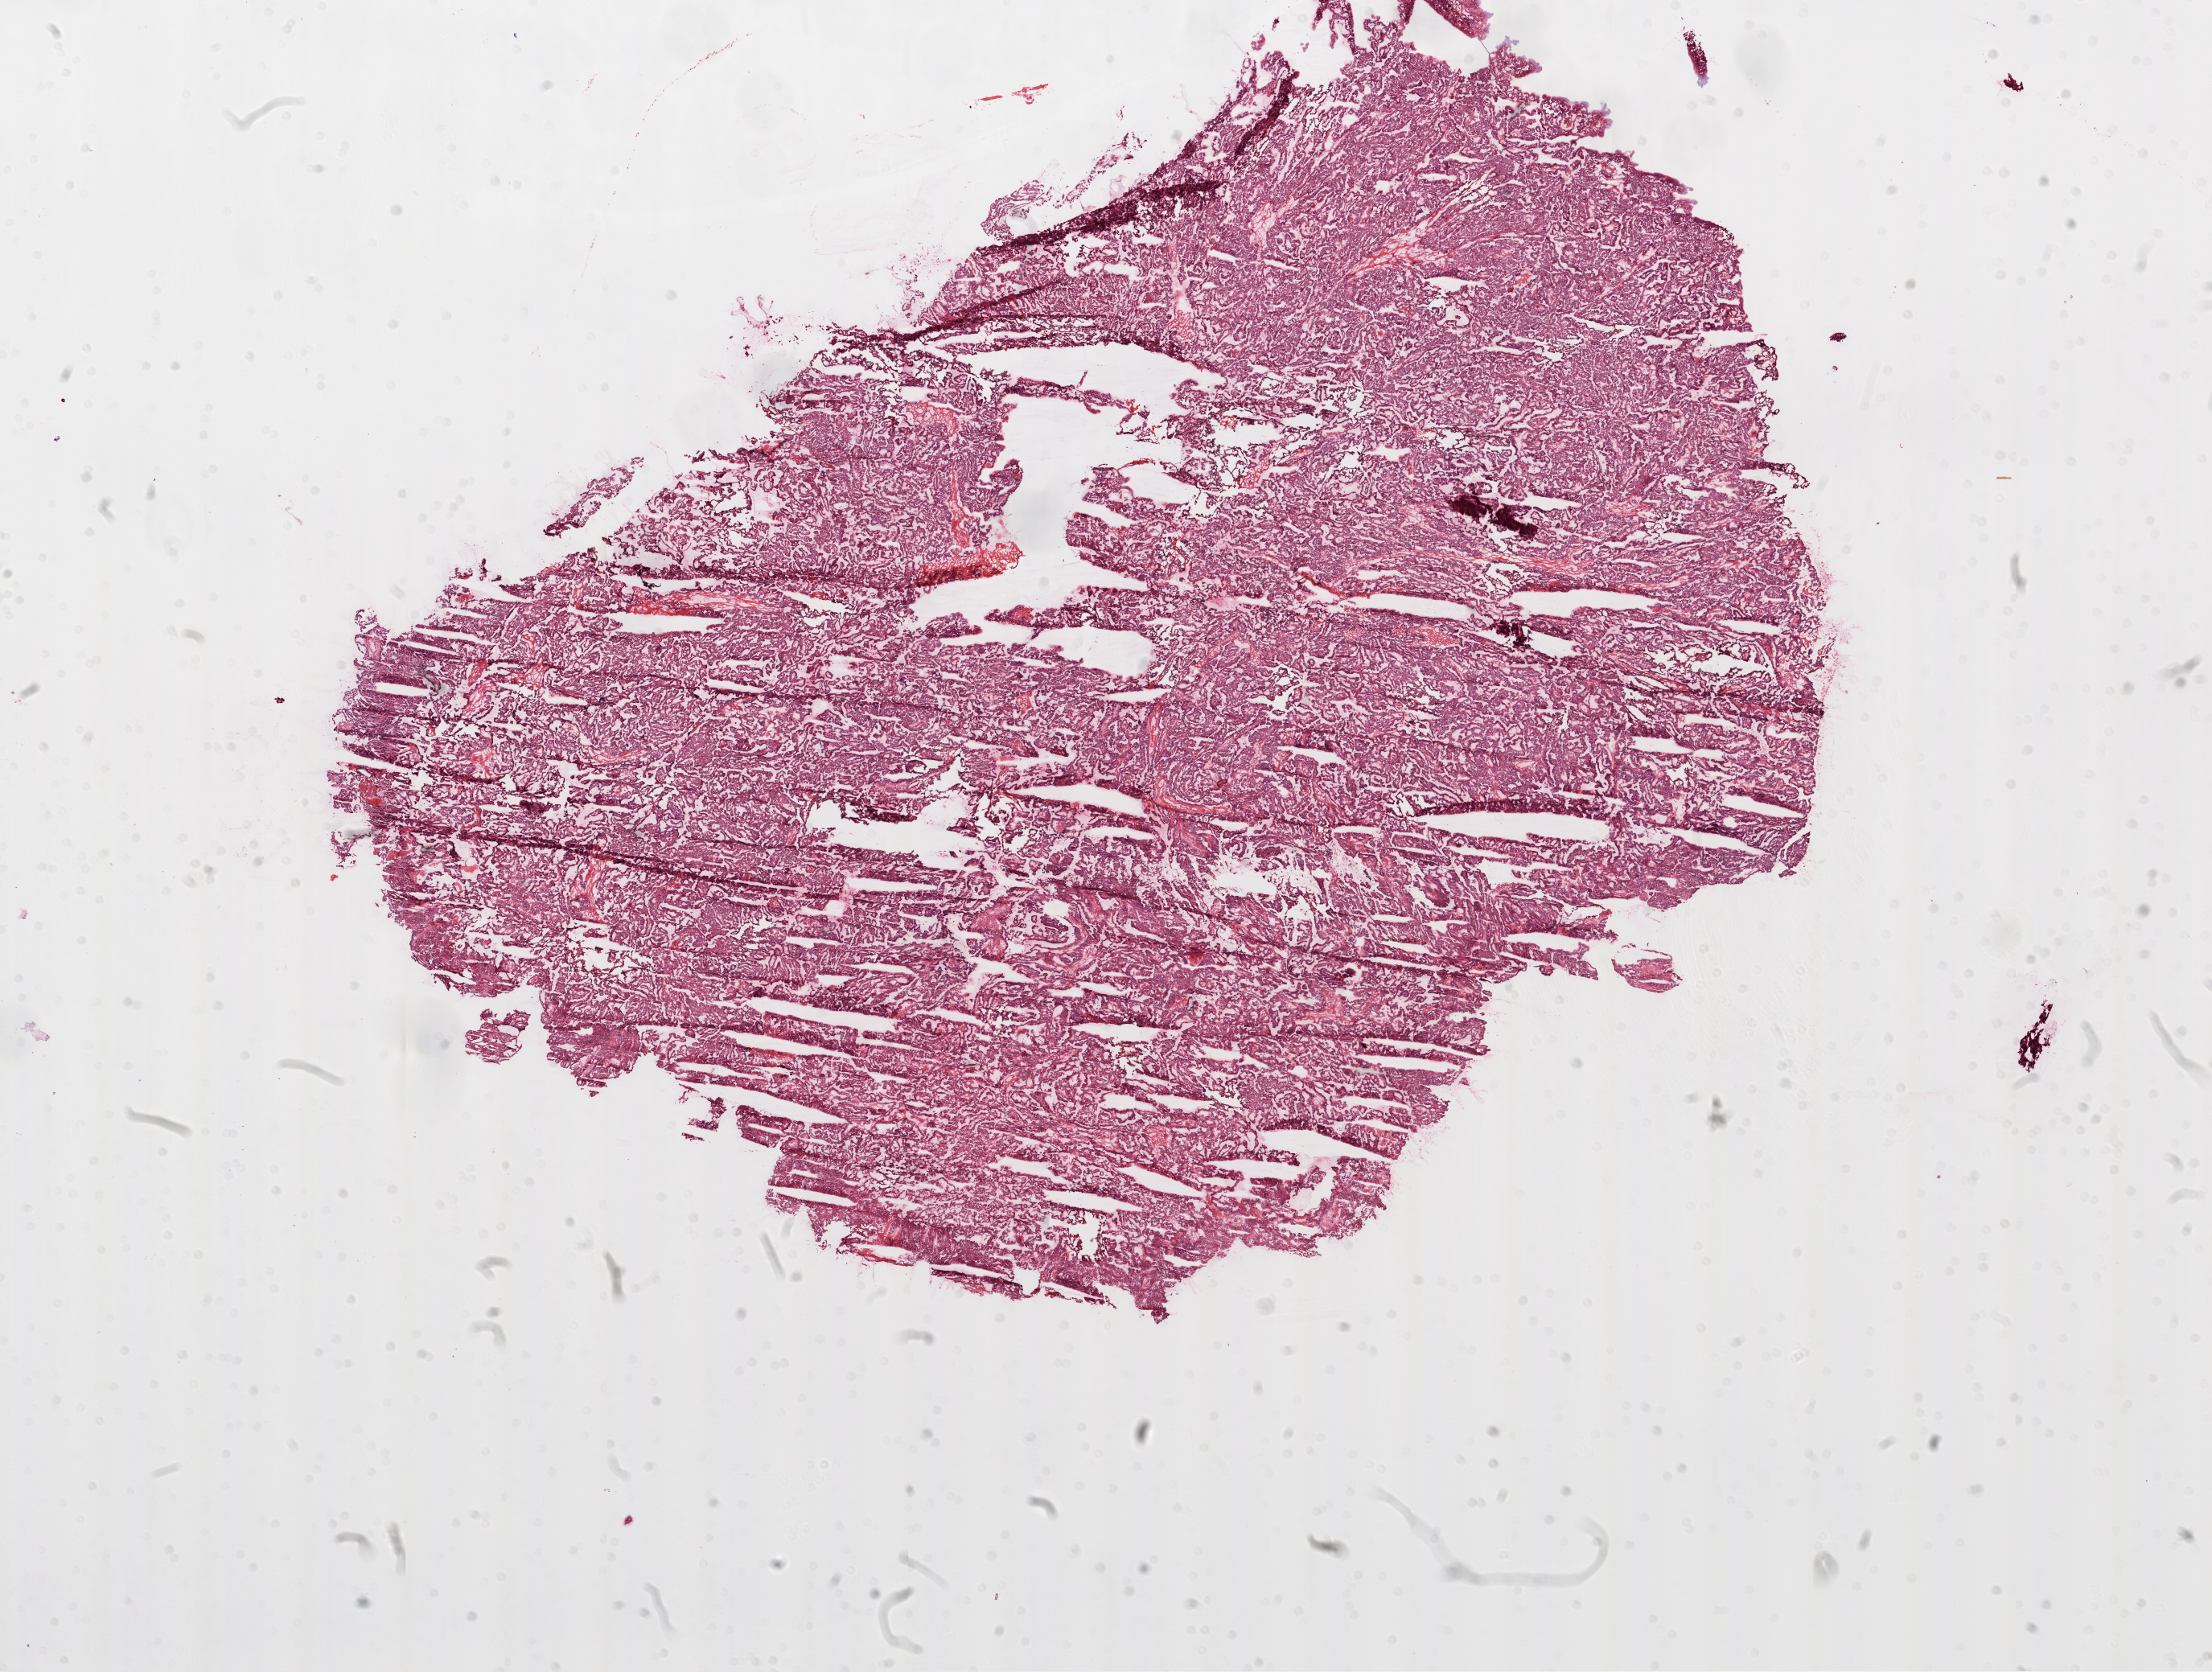
Digitized Hematoxylin and eosin (H&E) stained tissue section (whole slide), a low-resolution overview of the entire scanned area, about 22.1 x 16.7 mm (slide scanned at 20x). Frozen section from the top of the tissue portion. Sample: primary tumour, ovary. Female patient; age at initial diagnosis 51 years. Histologic grade: G3 (poorly differentiated). Pathologist review of this section (percent, as recorded): tumour cells 94%, tumour nuclei 95%, normal cells 0%, stromal cells 5%, necrosis 1%.
Laterality: bilateral. Diagnosis: Serous cystadenocarcinoma, NOS. FIGO stage: IIIC.